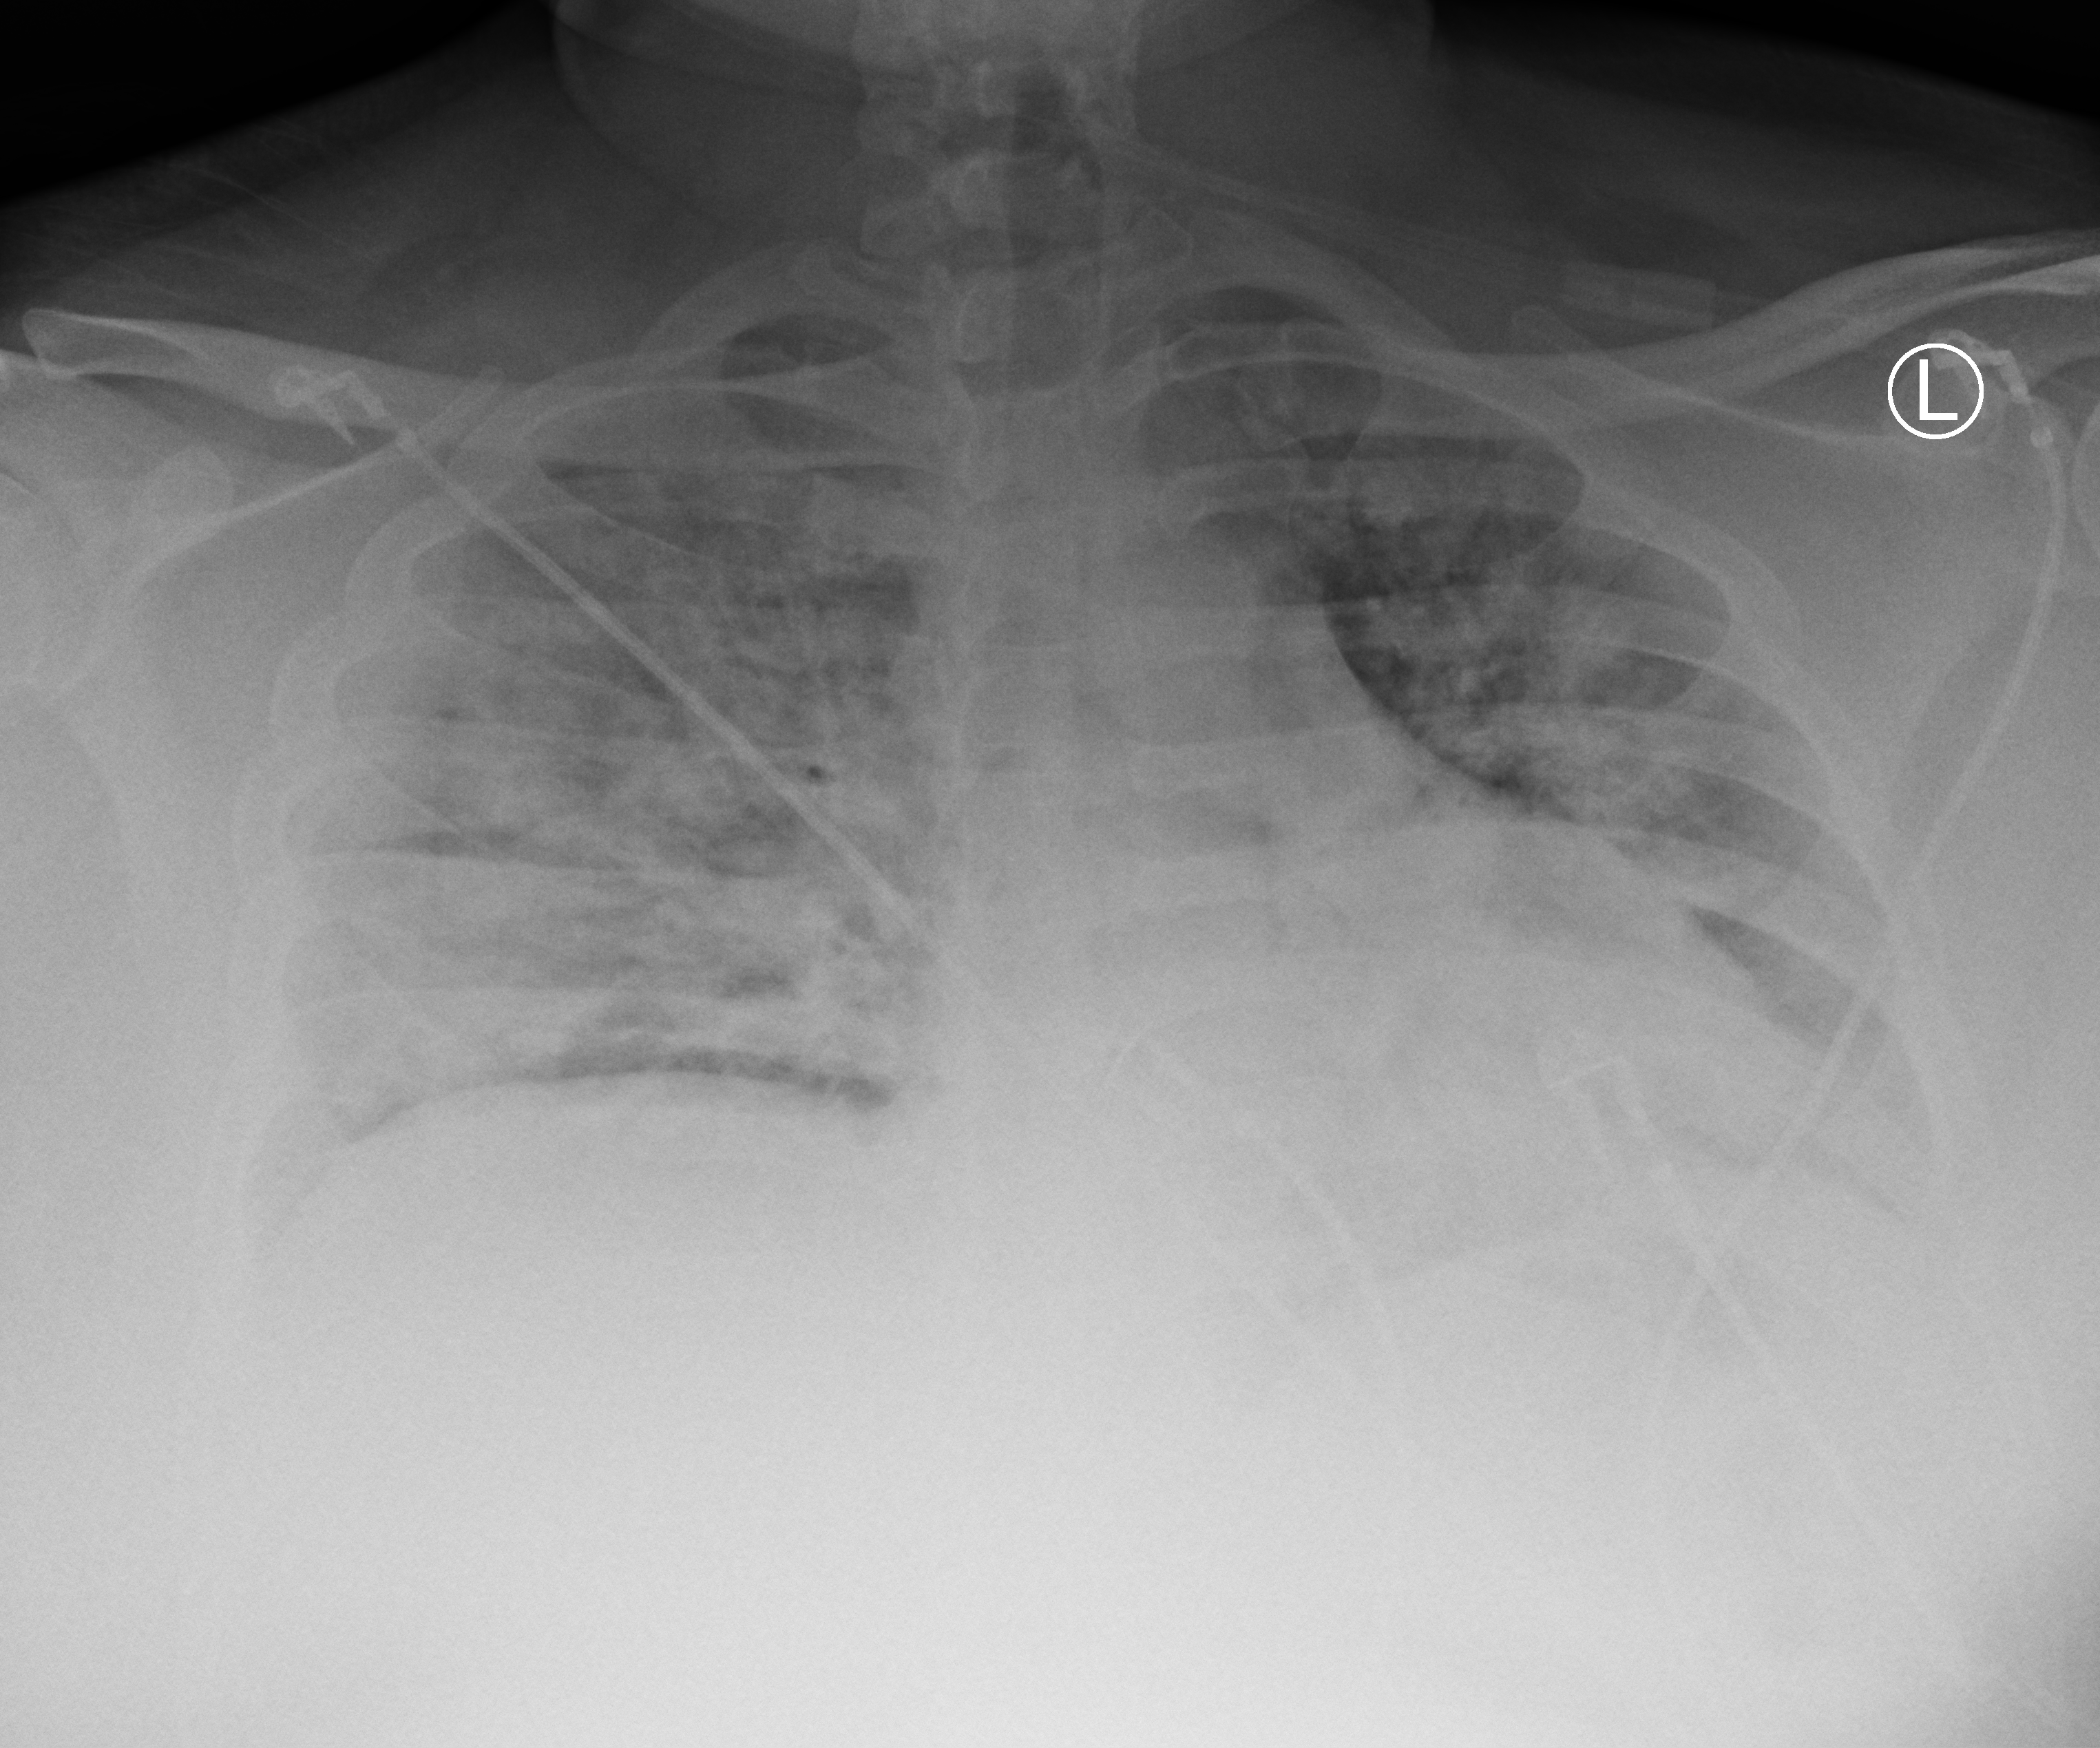
Chest X-ray (portable); anteroposterior (AP) projection. Male patient hospitalised with COVID-19, age 18–59 years.
Hospital-stay facts (about this admission, not read from this image; timing relative to this image not recorded): length of hospital stay: 69 days.